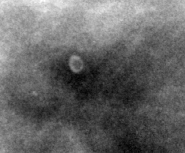
Crop from a digitized film mammogram around one marked abnormality; right breast; CC view.
- Calcifications, morphology lucent center; BI-RADS assessment category 2; benign without callback (not worked up further).